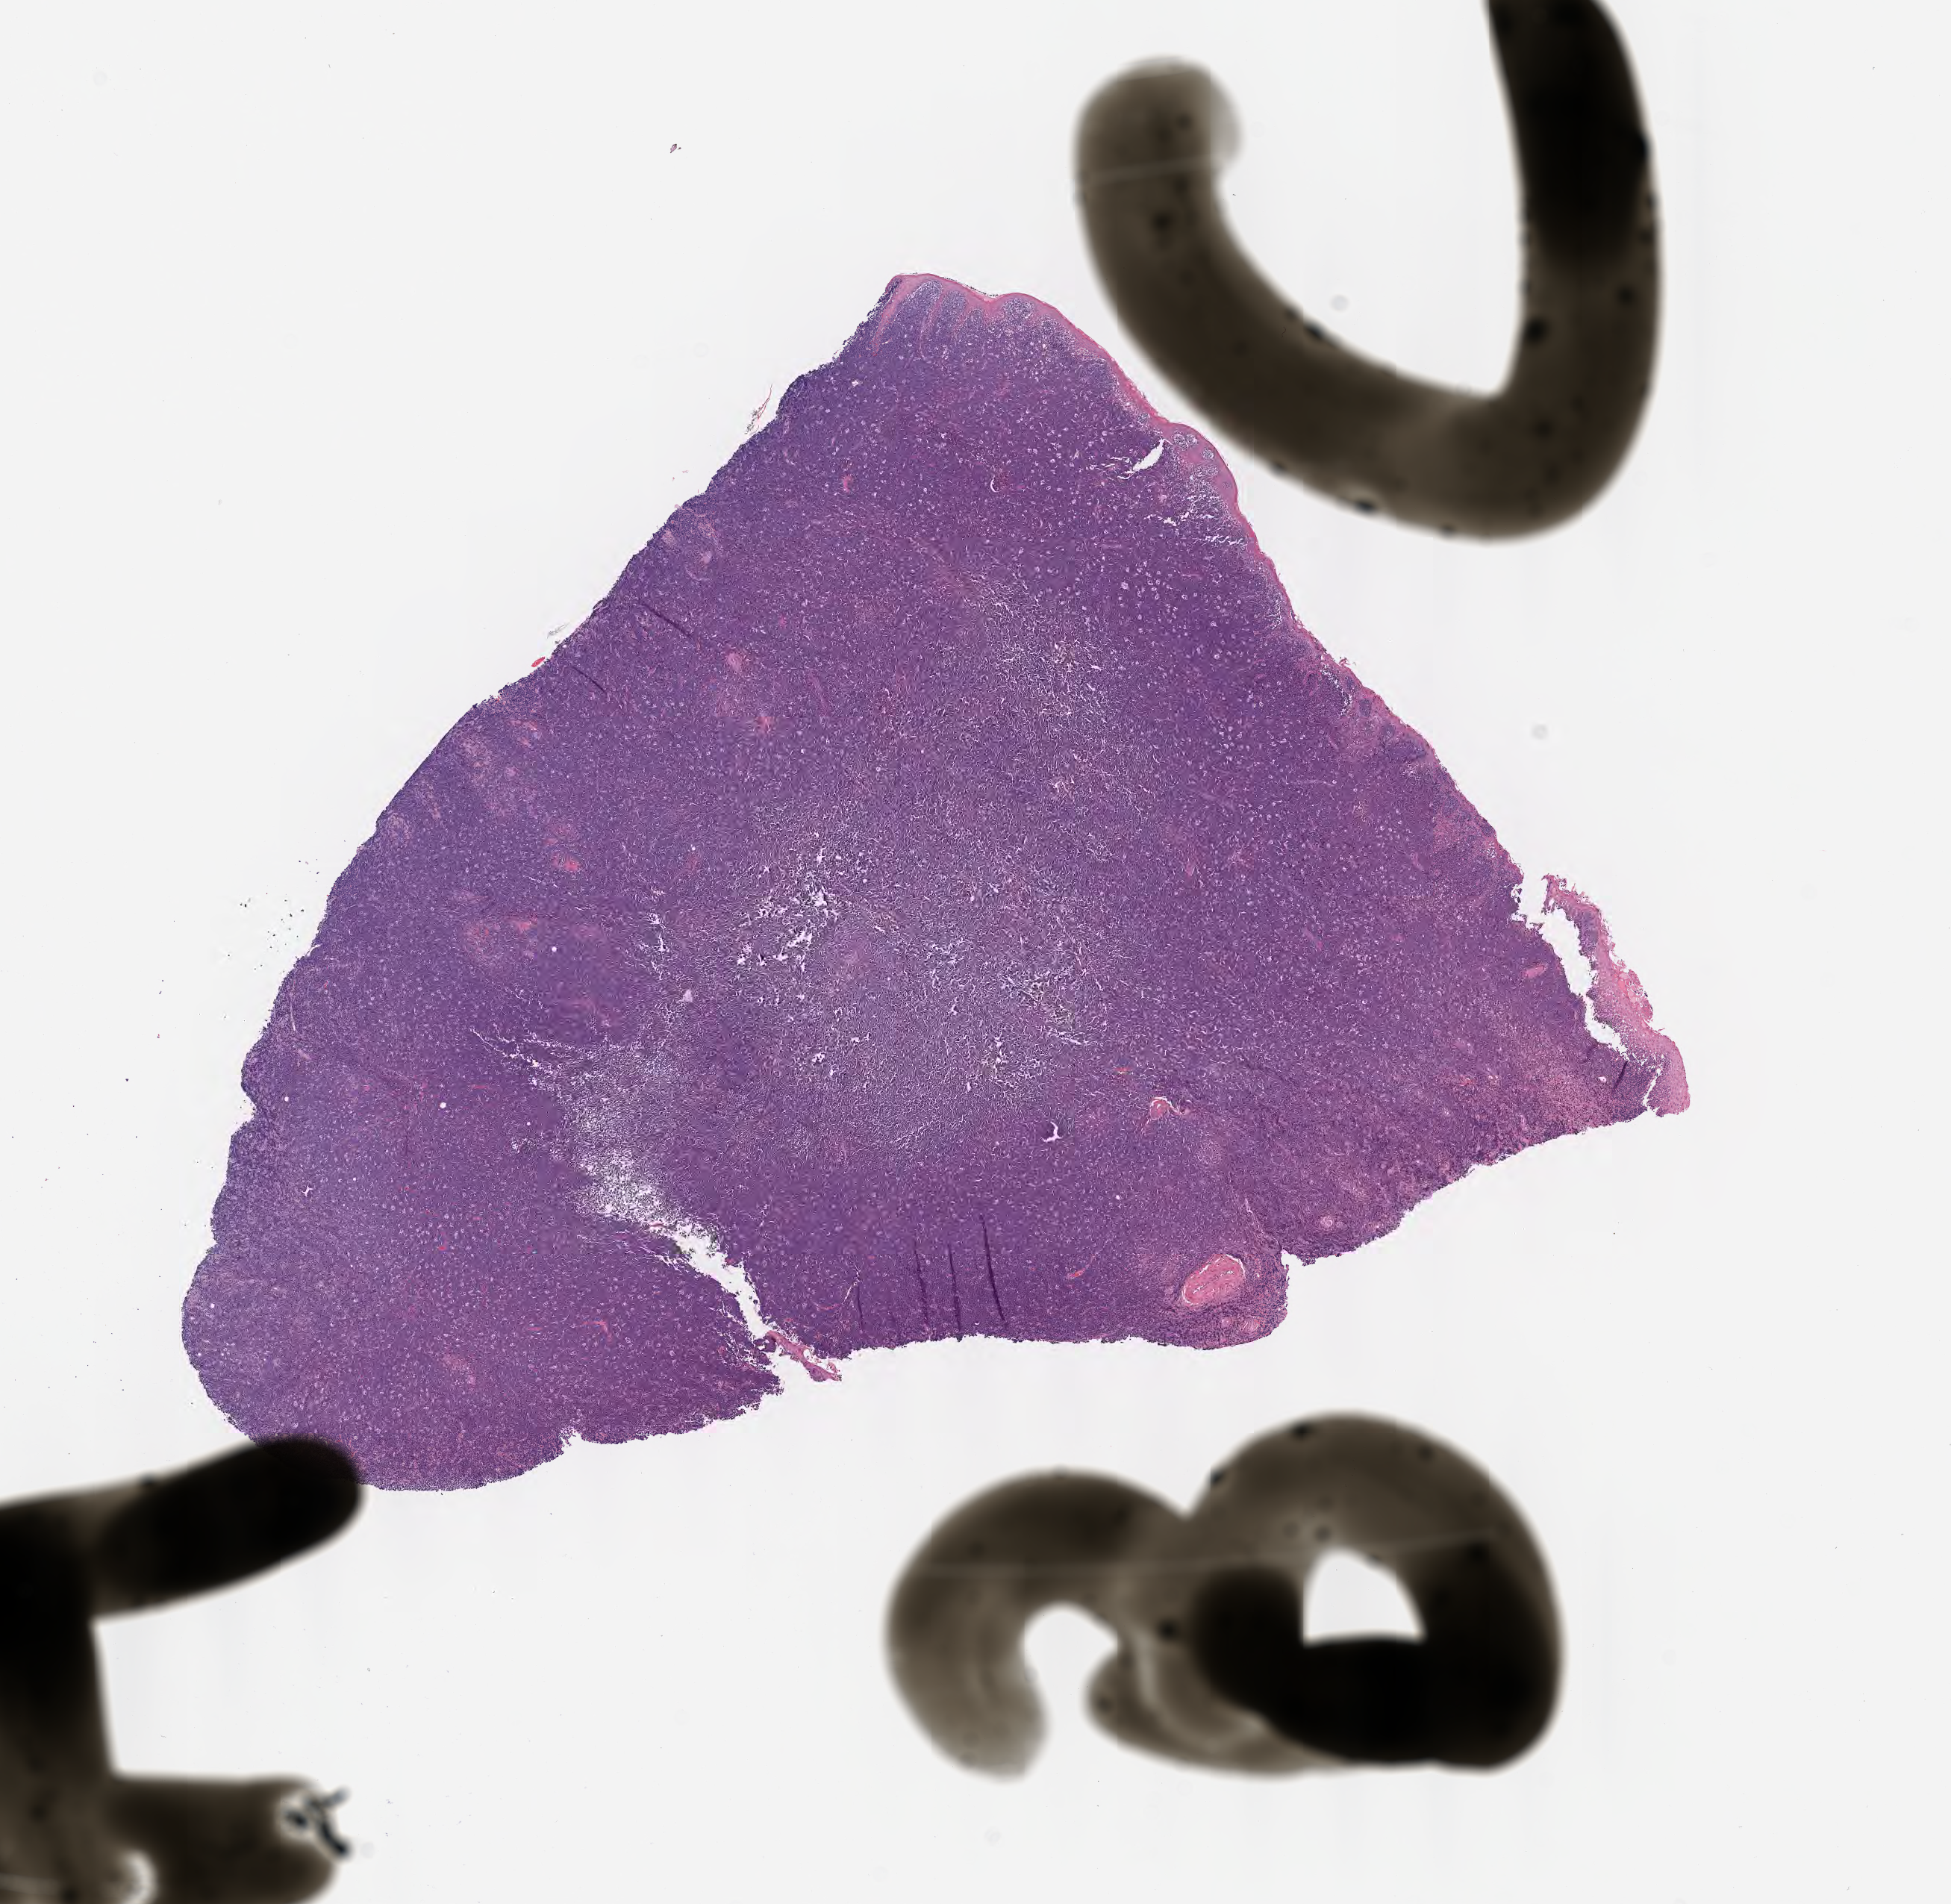
Digitized haematoxylin and eosin-stained section — whole scanned area (about 10.6 x 10.3 mm) shown as a low-resolution overview, specimen: tumor tissue, anatomic site: cranium. Male patient; age at initial diagnosis 8 years.
Diagnosis: Burkitt lymphoma, NOS.